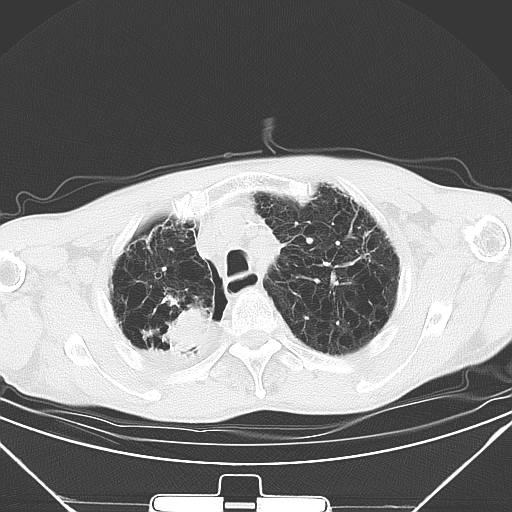
Chest CT, one axial slice; position 40 of 50 along the scan axis; lung window (W 1500 / L -600 HU); 5 mm slice thickness; 512 × 512 image matrix, field of view 373 × 373 mm. Patient: male, 65 years. Case-level facts recorded for this patient, not image findings: clinical TNM (as recorded): T3 N1 M1a.
Outlined on this slice (rectangle marked by the reading radiologist):
- lung tumour (recorded histology: squamous cell carcinoma): bounding box [x1, y1, x2, y2] px = [162, 303, 213, 353]